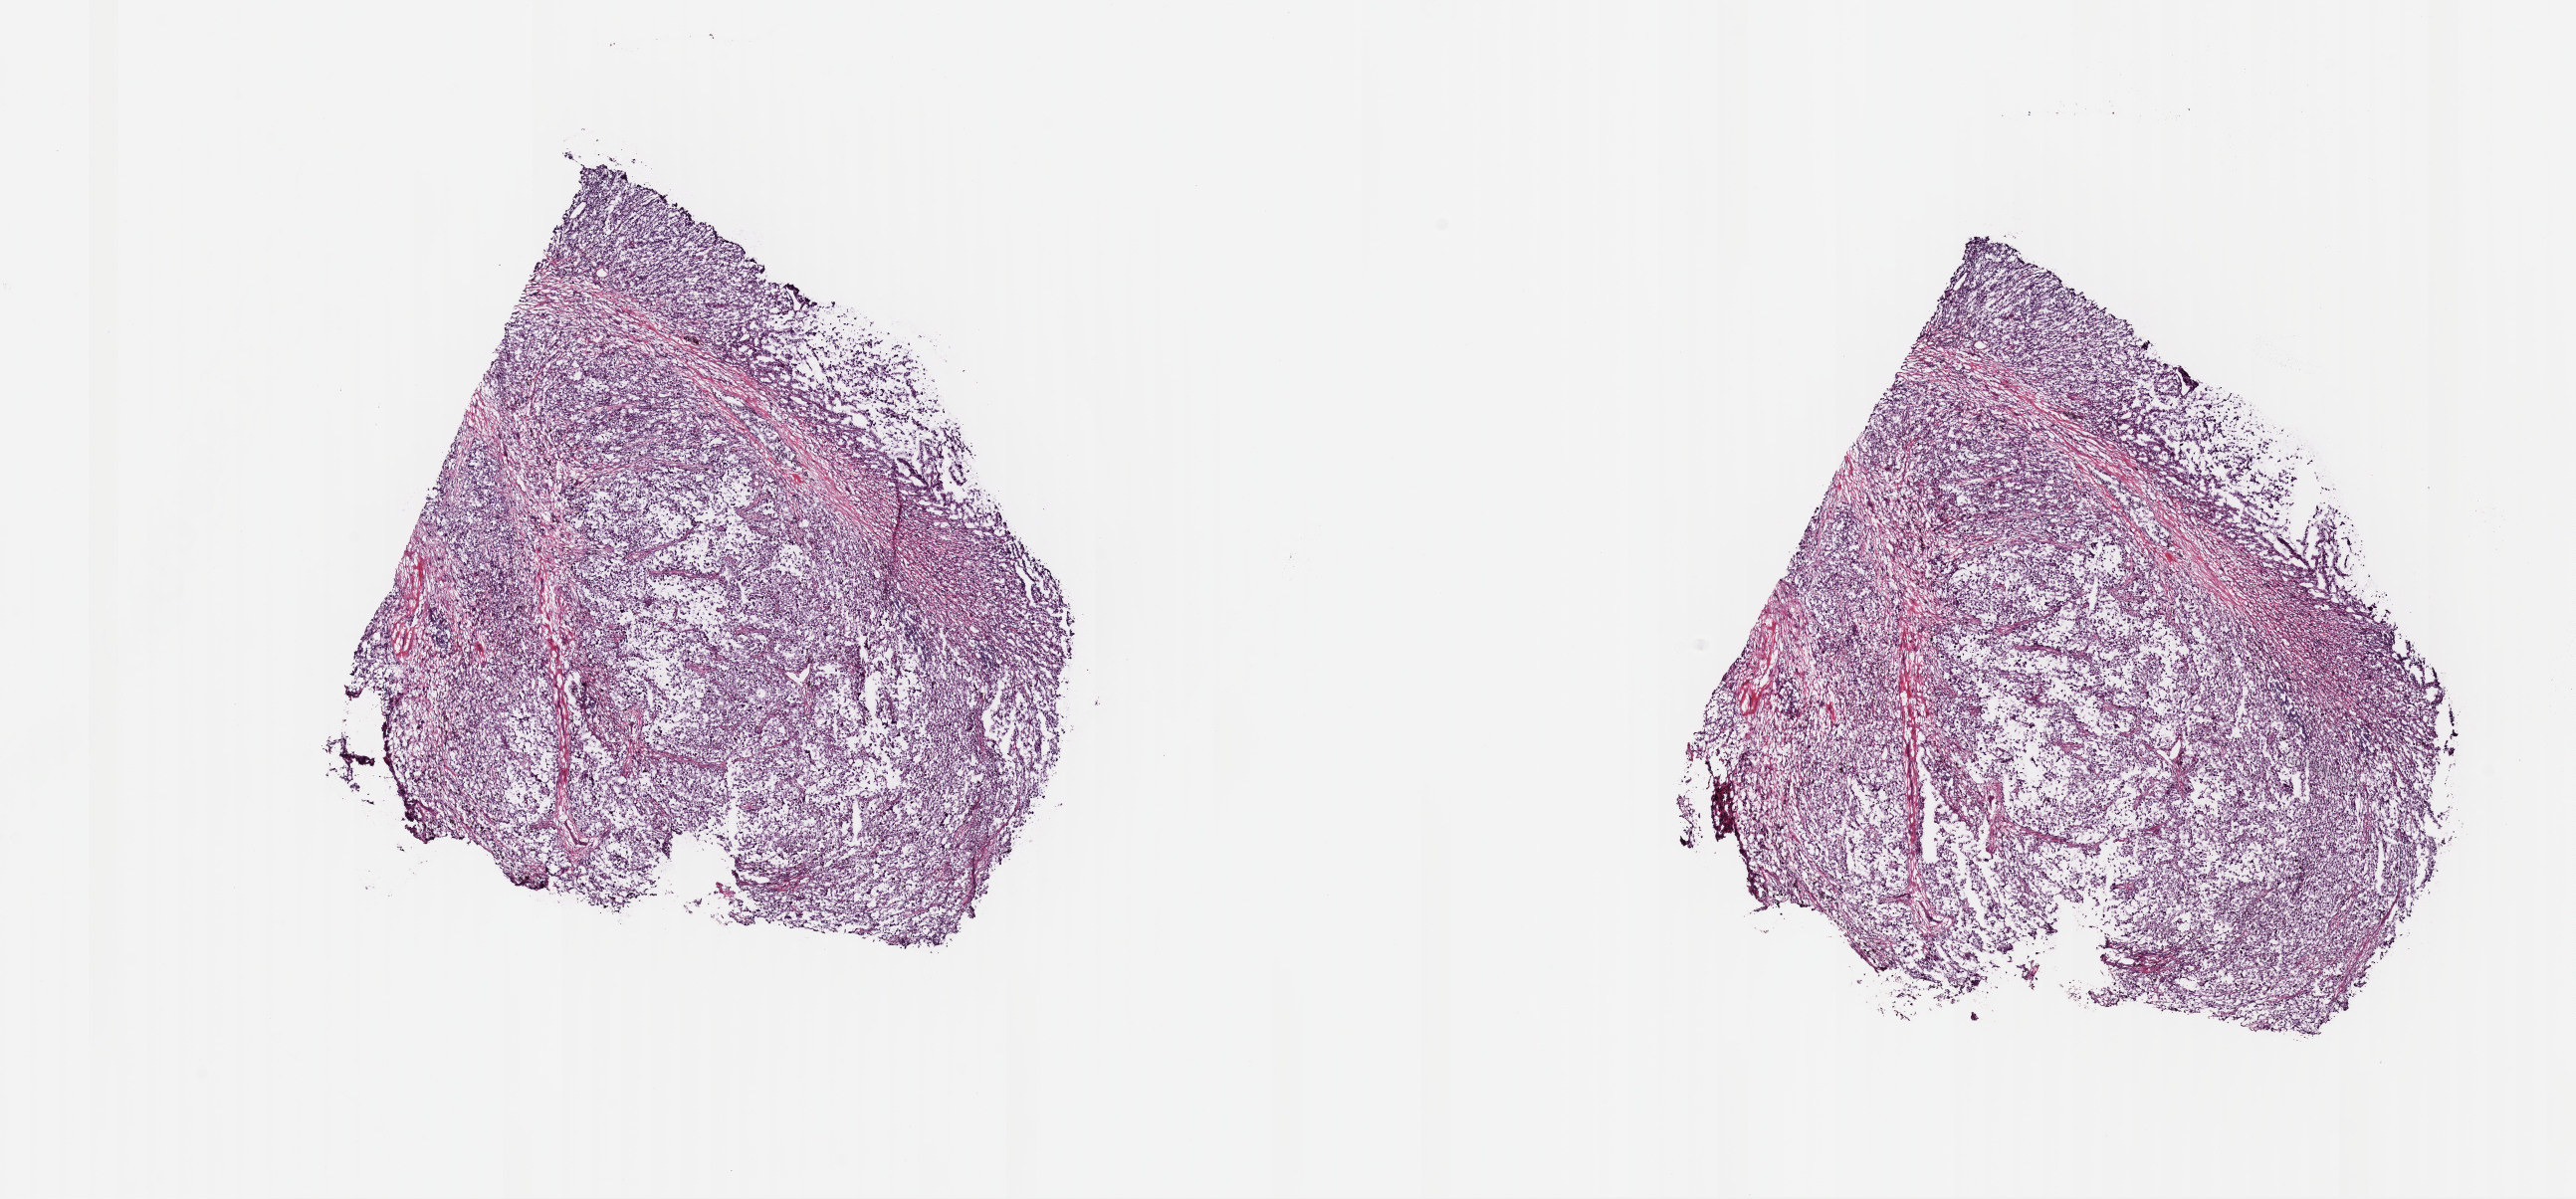
Digitized H&E tissue section (whole slide), low-resolution overview of the scanned area, about 20.4 x 9.5 mm (from a 40x scan), frozen section, metastatic tumour sample, sampled site not recorded. Patient sex: male. Pathologist review of this section (percent, as recorded): tumour cells 90%, tumour nuclei 90%, normal cells 5%, stromal cells 3%, necrosis 2%. Infiltration values recorded for this section: lymphocyte infiltration 1%, monocyte infiltration 3%, neutrophil infiltration 0%.
This section: metastatic tumour tissue. Patient diagnosis: Malignant melanoma, NOS.